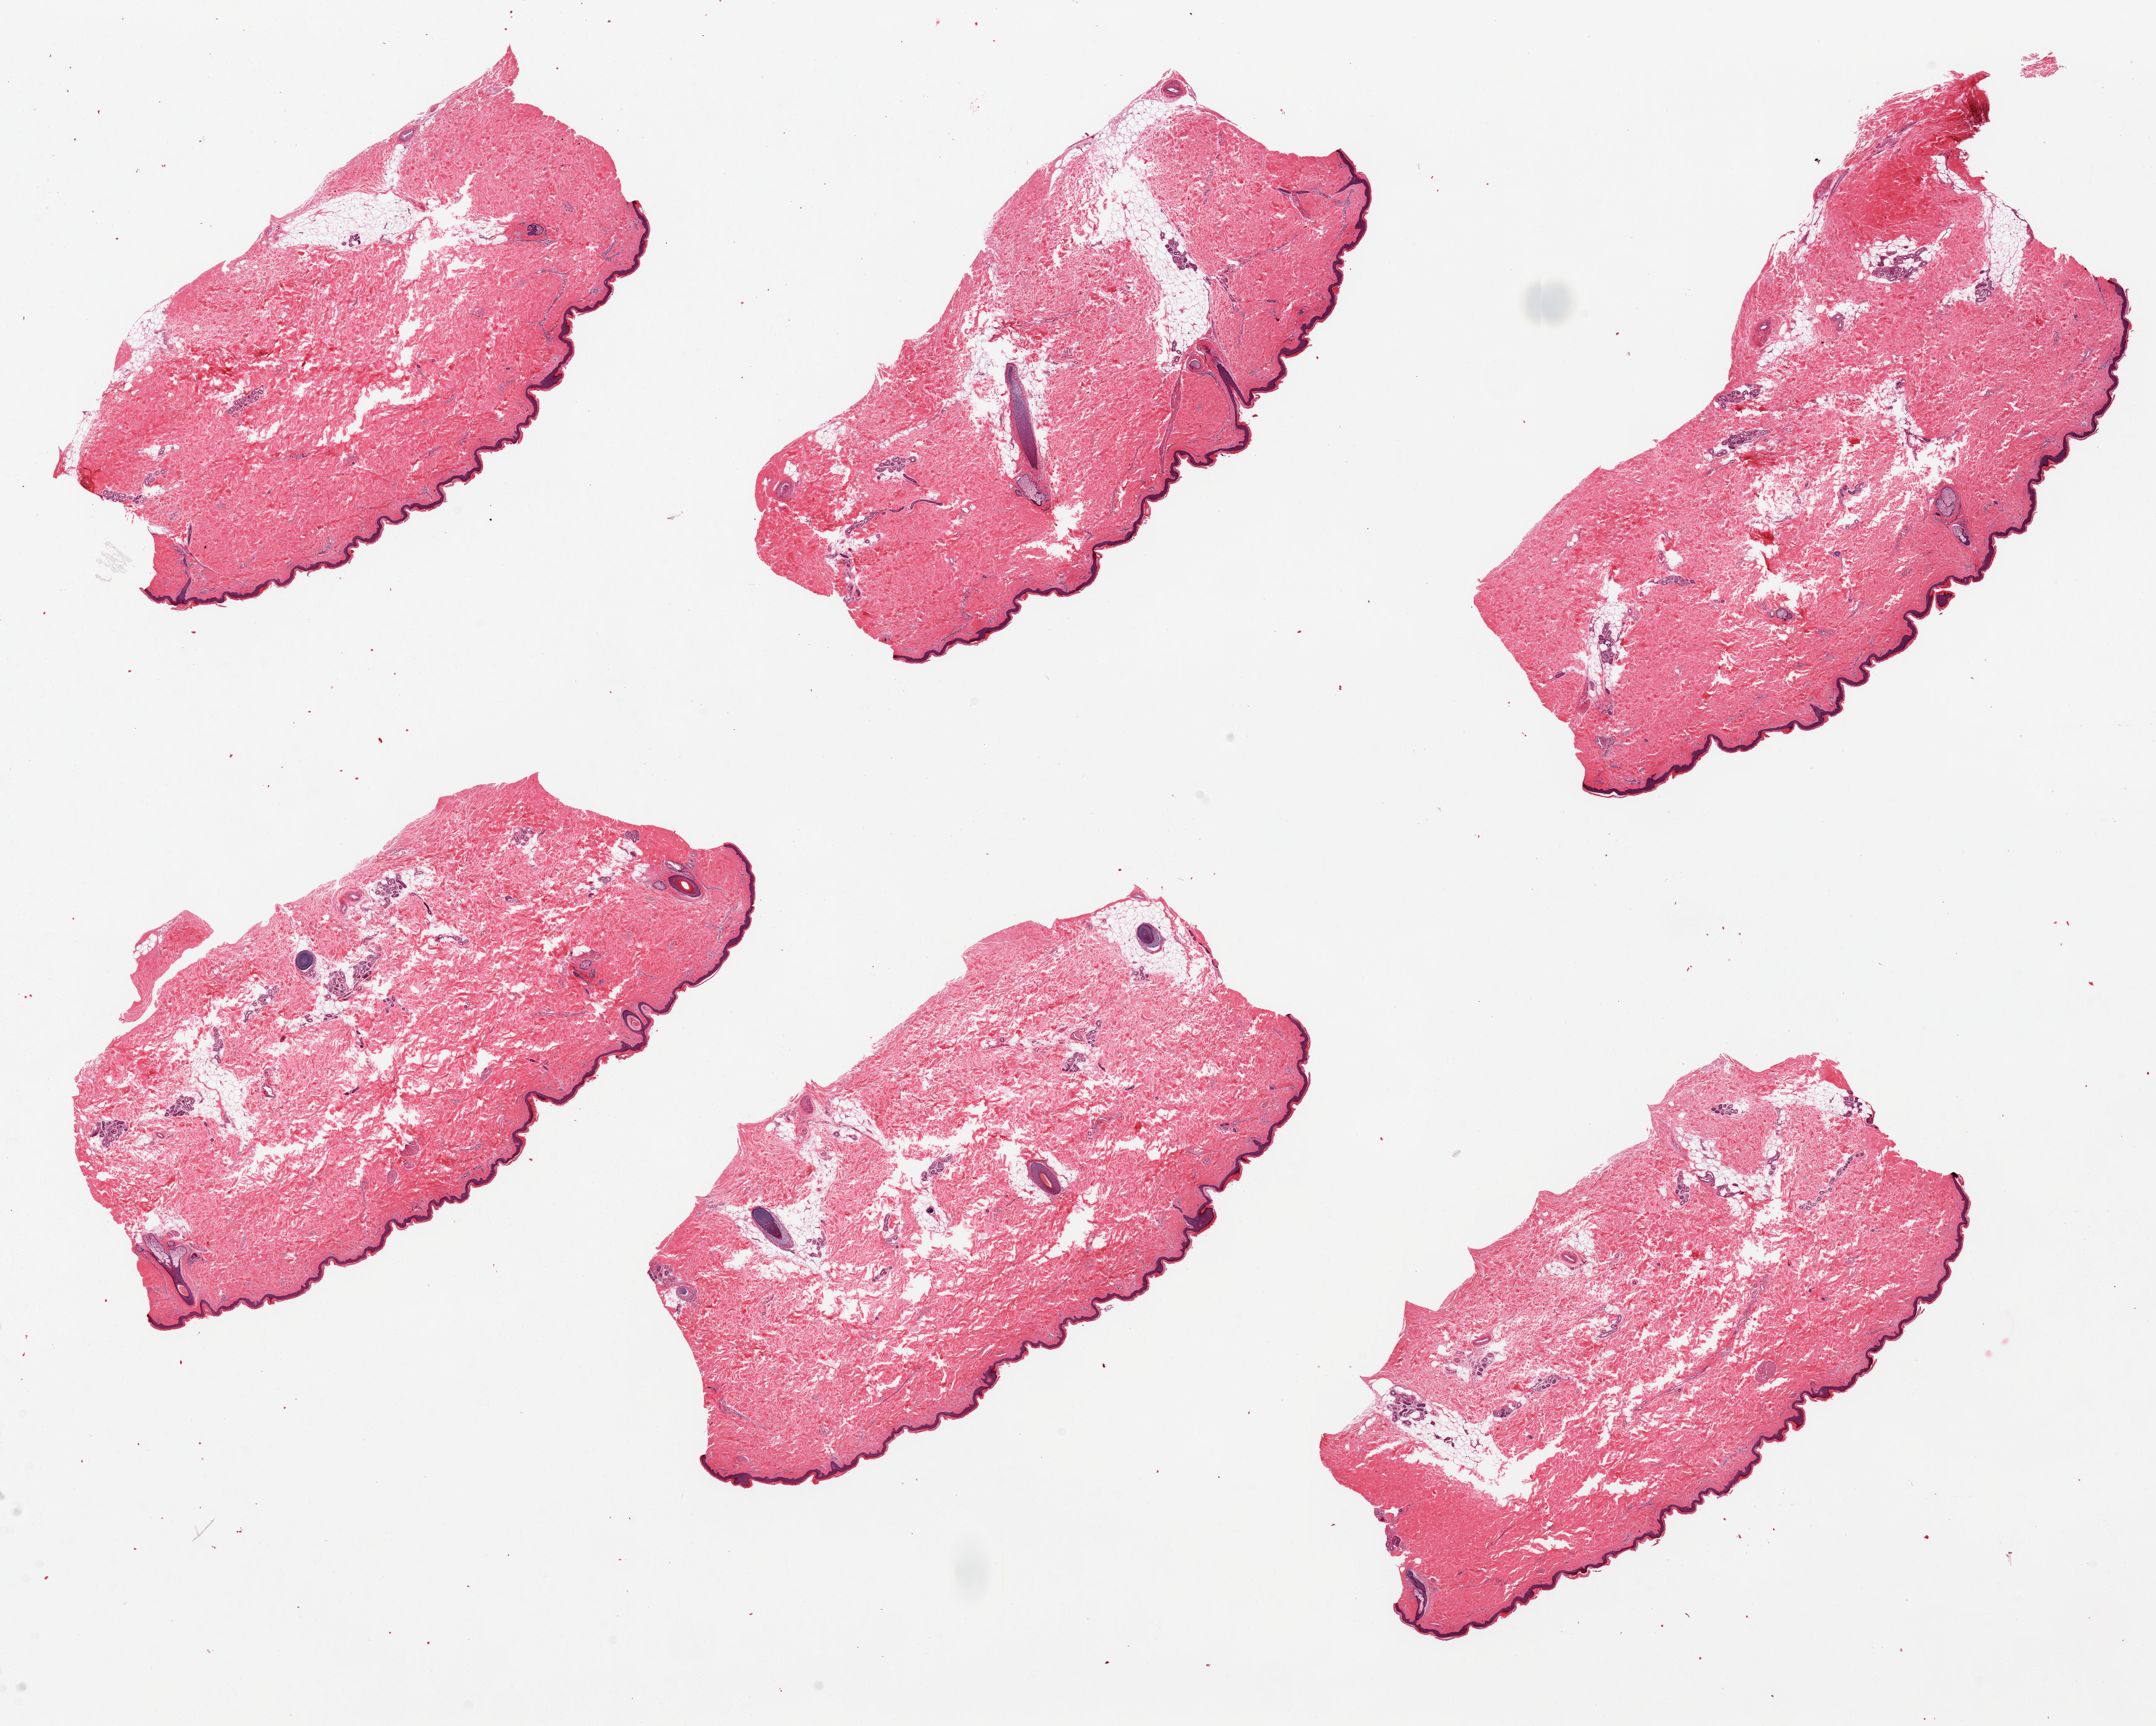
Hematoxylin and eosin (H&E) whole-slide image — a low-resolution overview of the entire scanned area, about 27.6 x 22.1 mm (acquisition: 20x scan). PAXgene-fixed paraffin-embedded (PFPE) section. Target tissue: skin of lower leg. Tissue donor sample. Donor: male.
Review note (as recorded): 6 pieces, no dermal fat; squamous epithelium is ~50 microns.